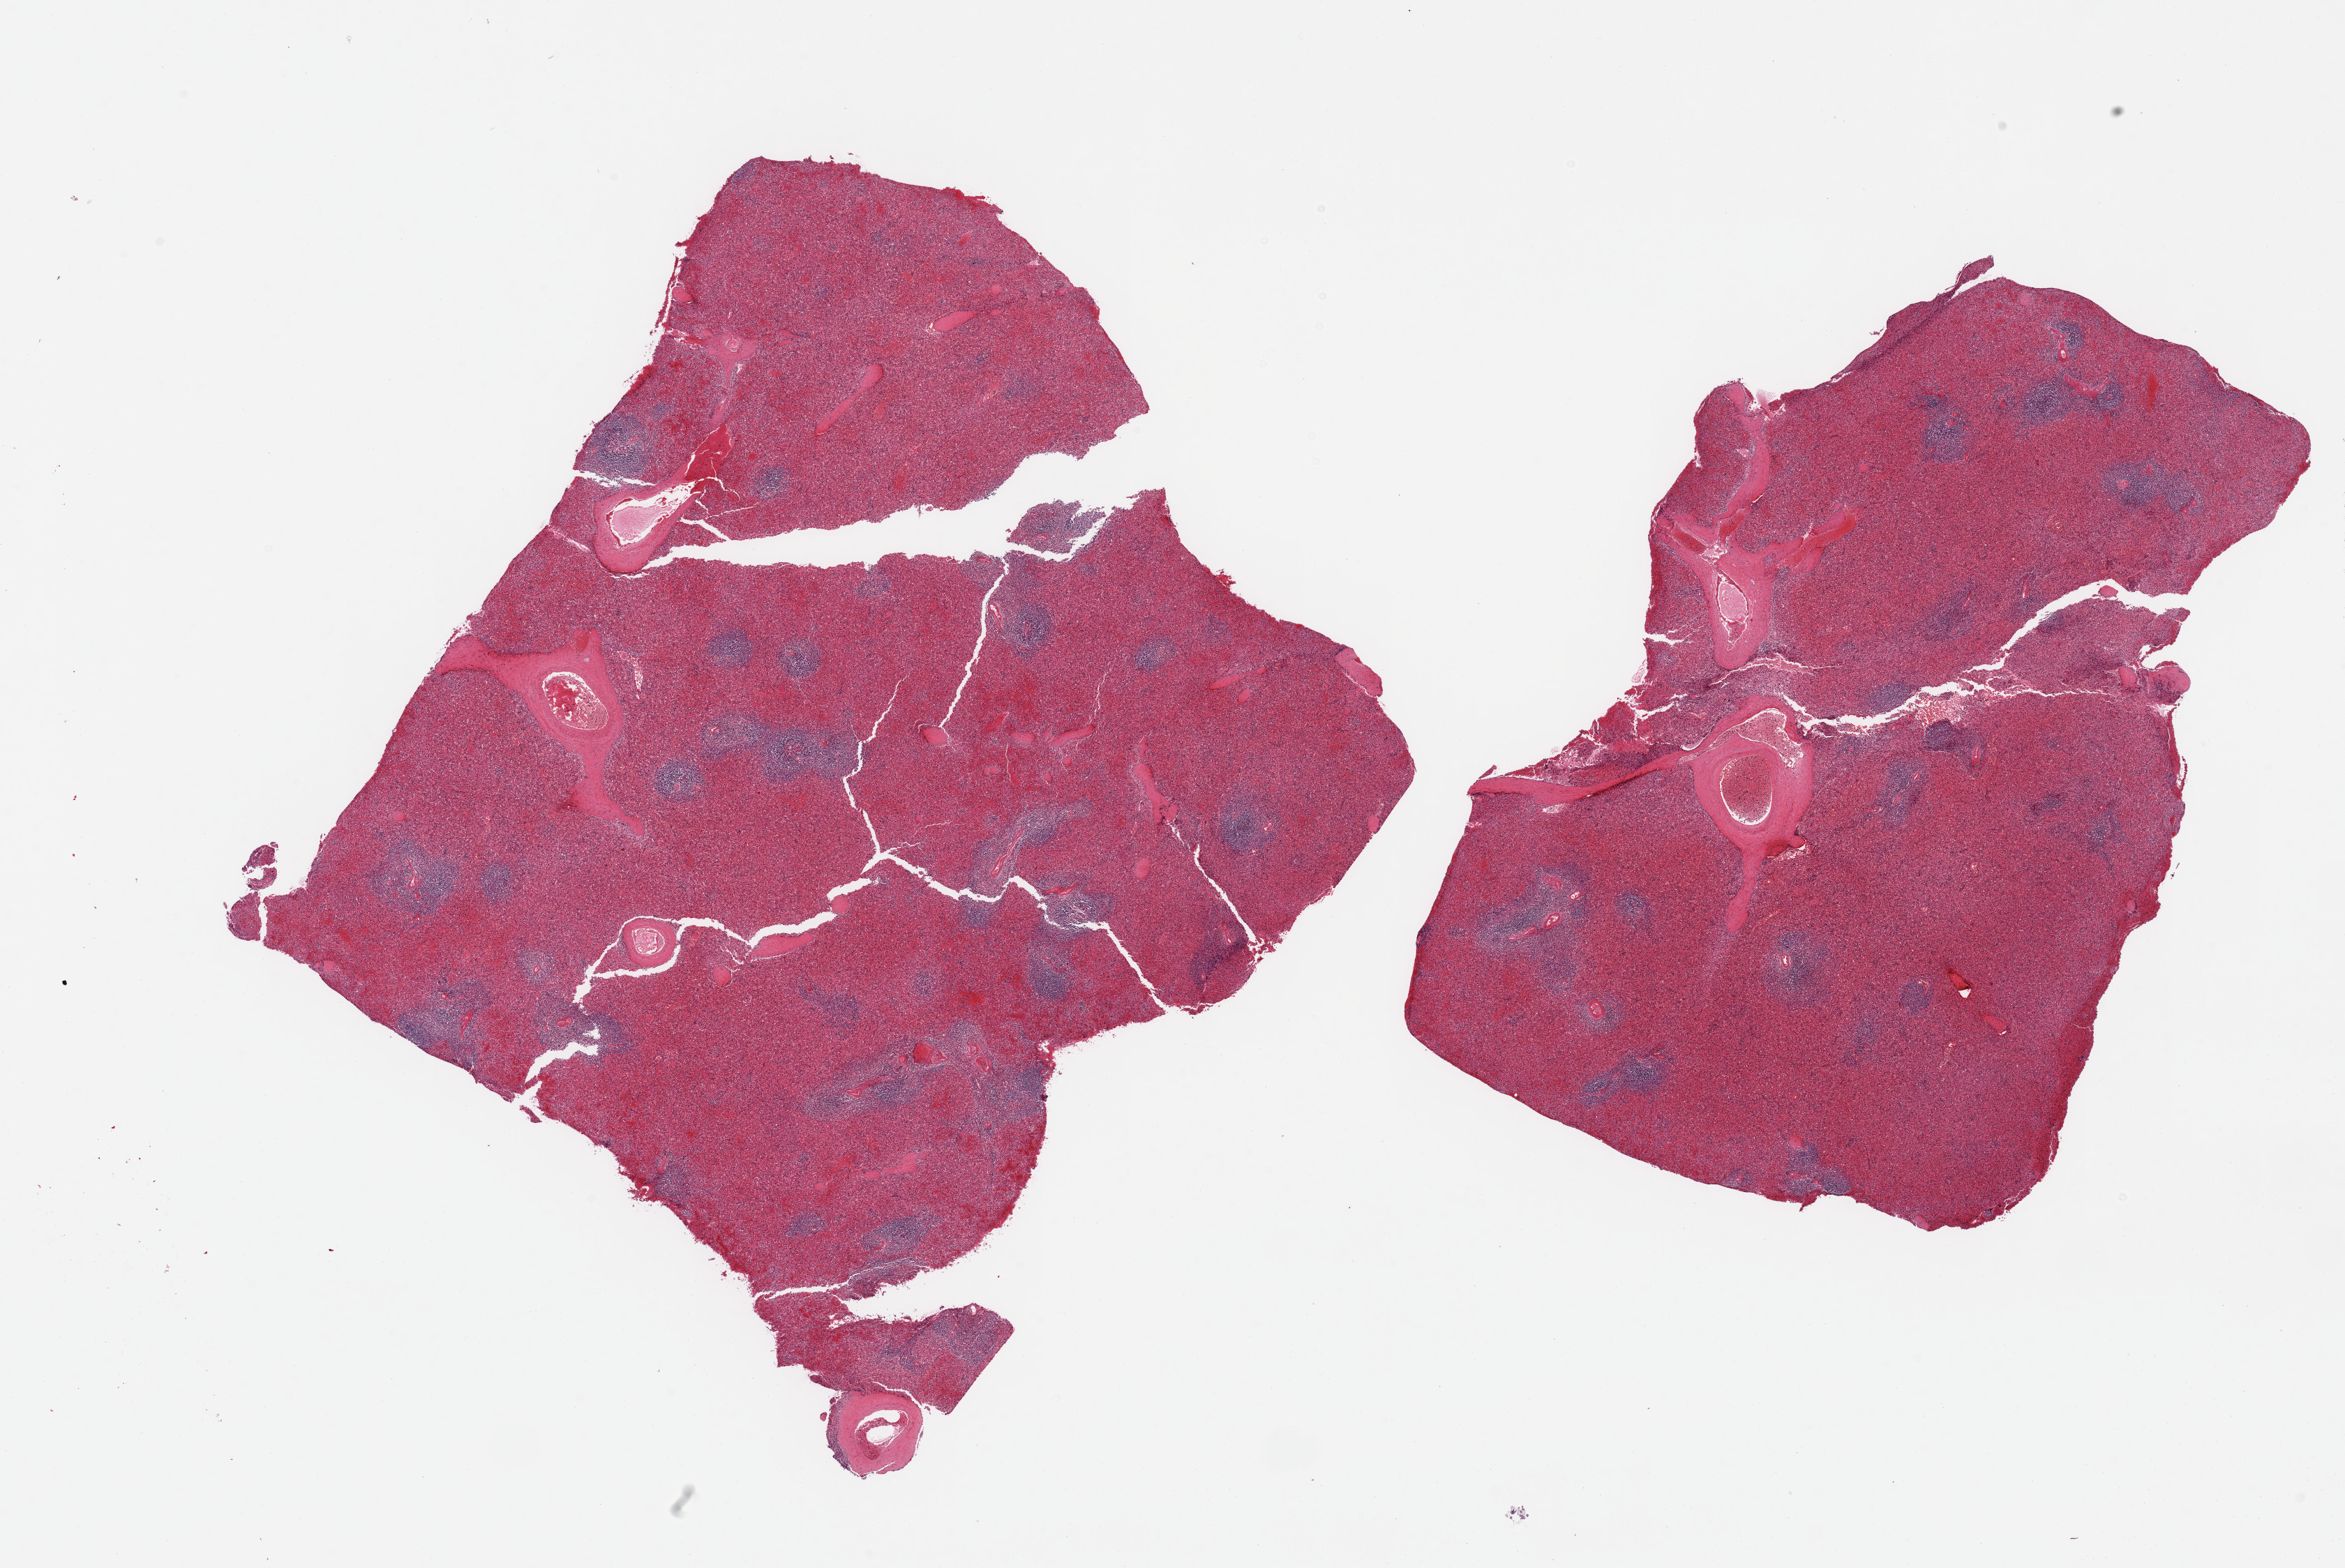
Haematoxylin and eosin whole-slide image, brightfield — low-resolution overview of the scanned area, about 26.6 x 17.8 mm, PAXgene-fixed paraffin-embedded (PFPE) section, section of spleen (target tissue), donor tissue sample. Donor: male.
Pathologist's review note for this sample: 2 pieces, moderate-makred congestion.